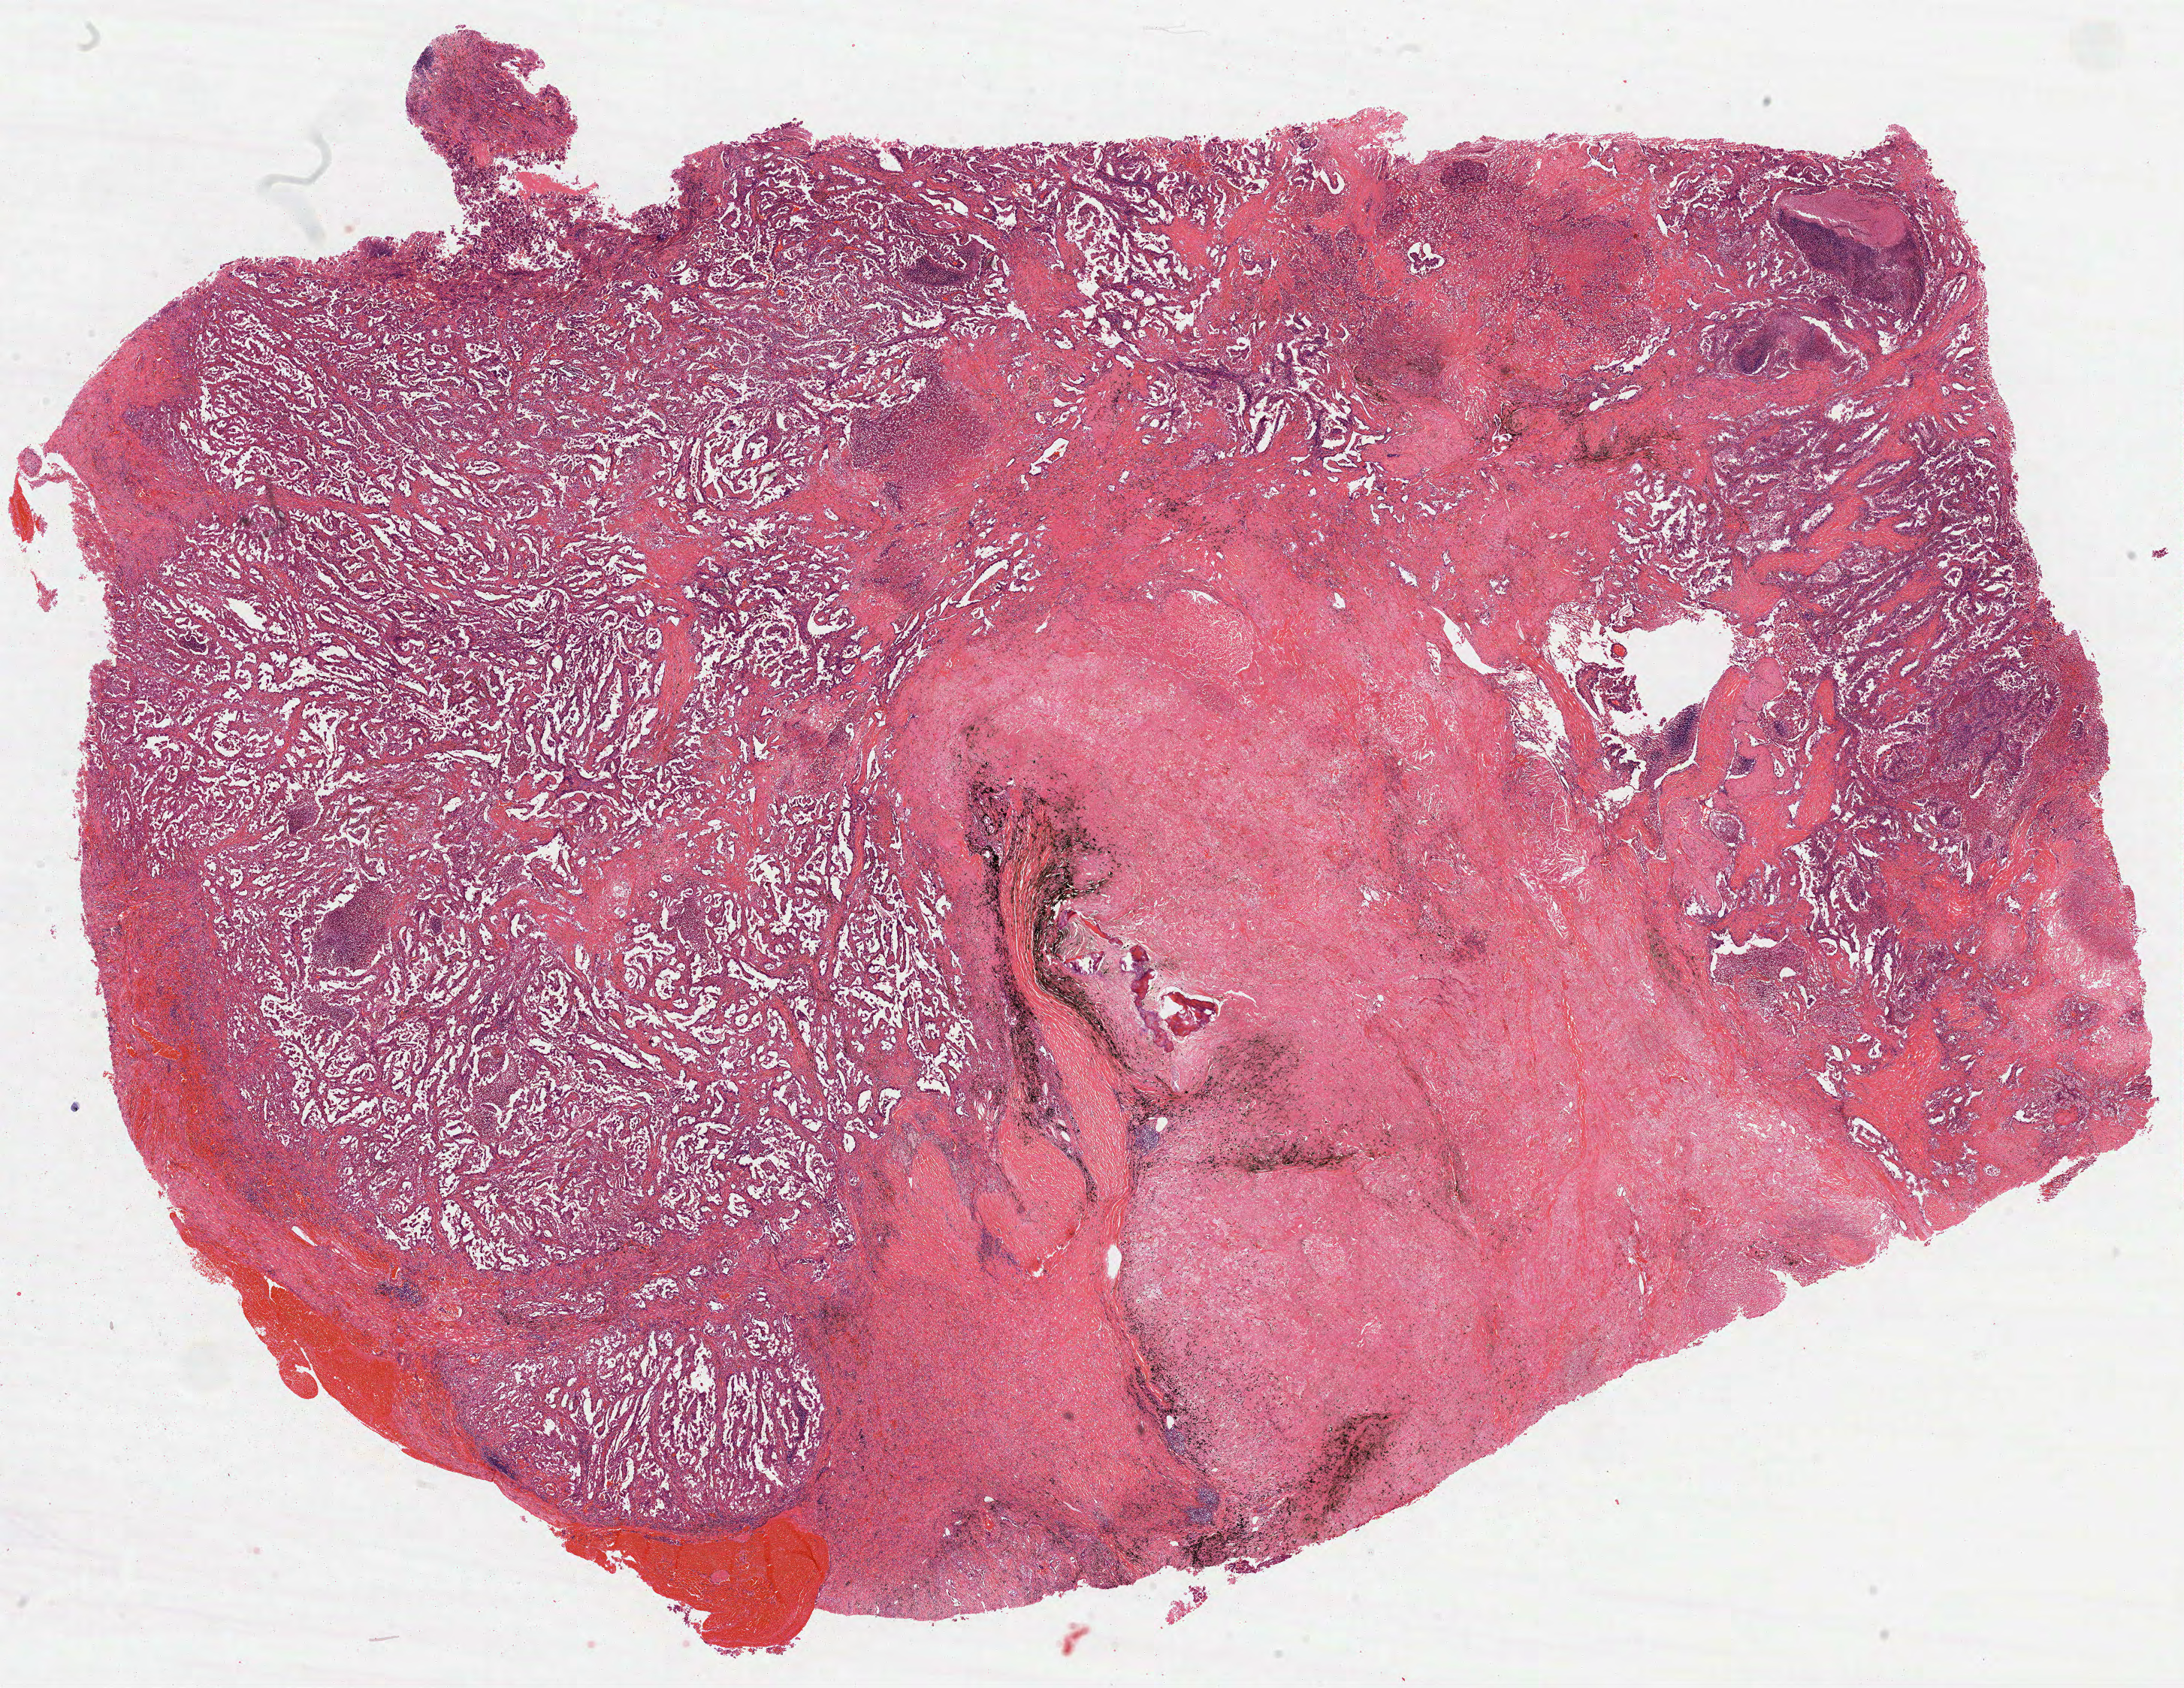
Whole-slide histology image, H&E — whole scanned area (about 23.4 x 18.1 mm, slide scanned at 40x) shown as a low-resolution overview, formalin-fixed paraffin-embedded (FFPE) diagnostic section, sample: primary tumour, lung. Patient: male, age at initial diagnosis 61 years.
* AJCC pathologic stage: IB (7th edition)
* diagnosis: Bronchiolo-alveolar carcinoma, non-mucinous (upper lobe, lung)